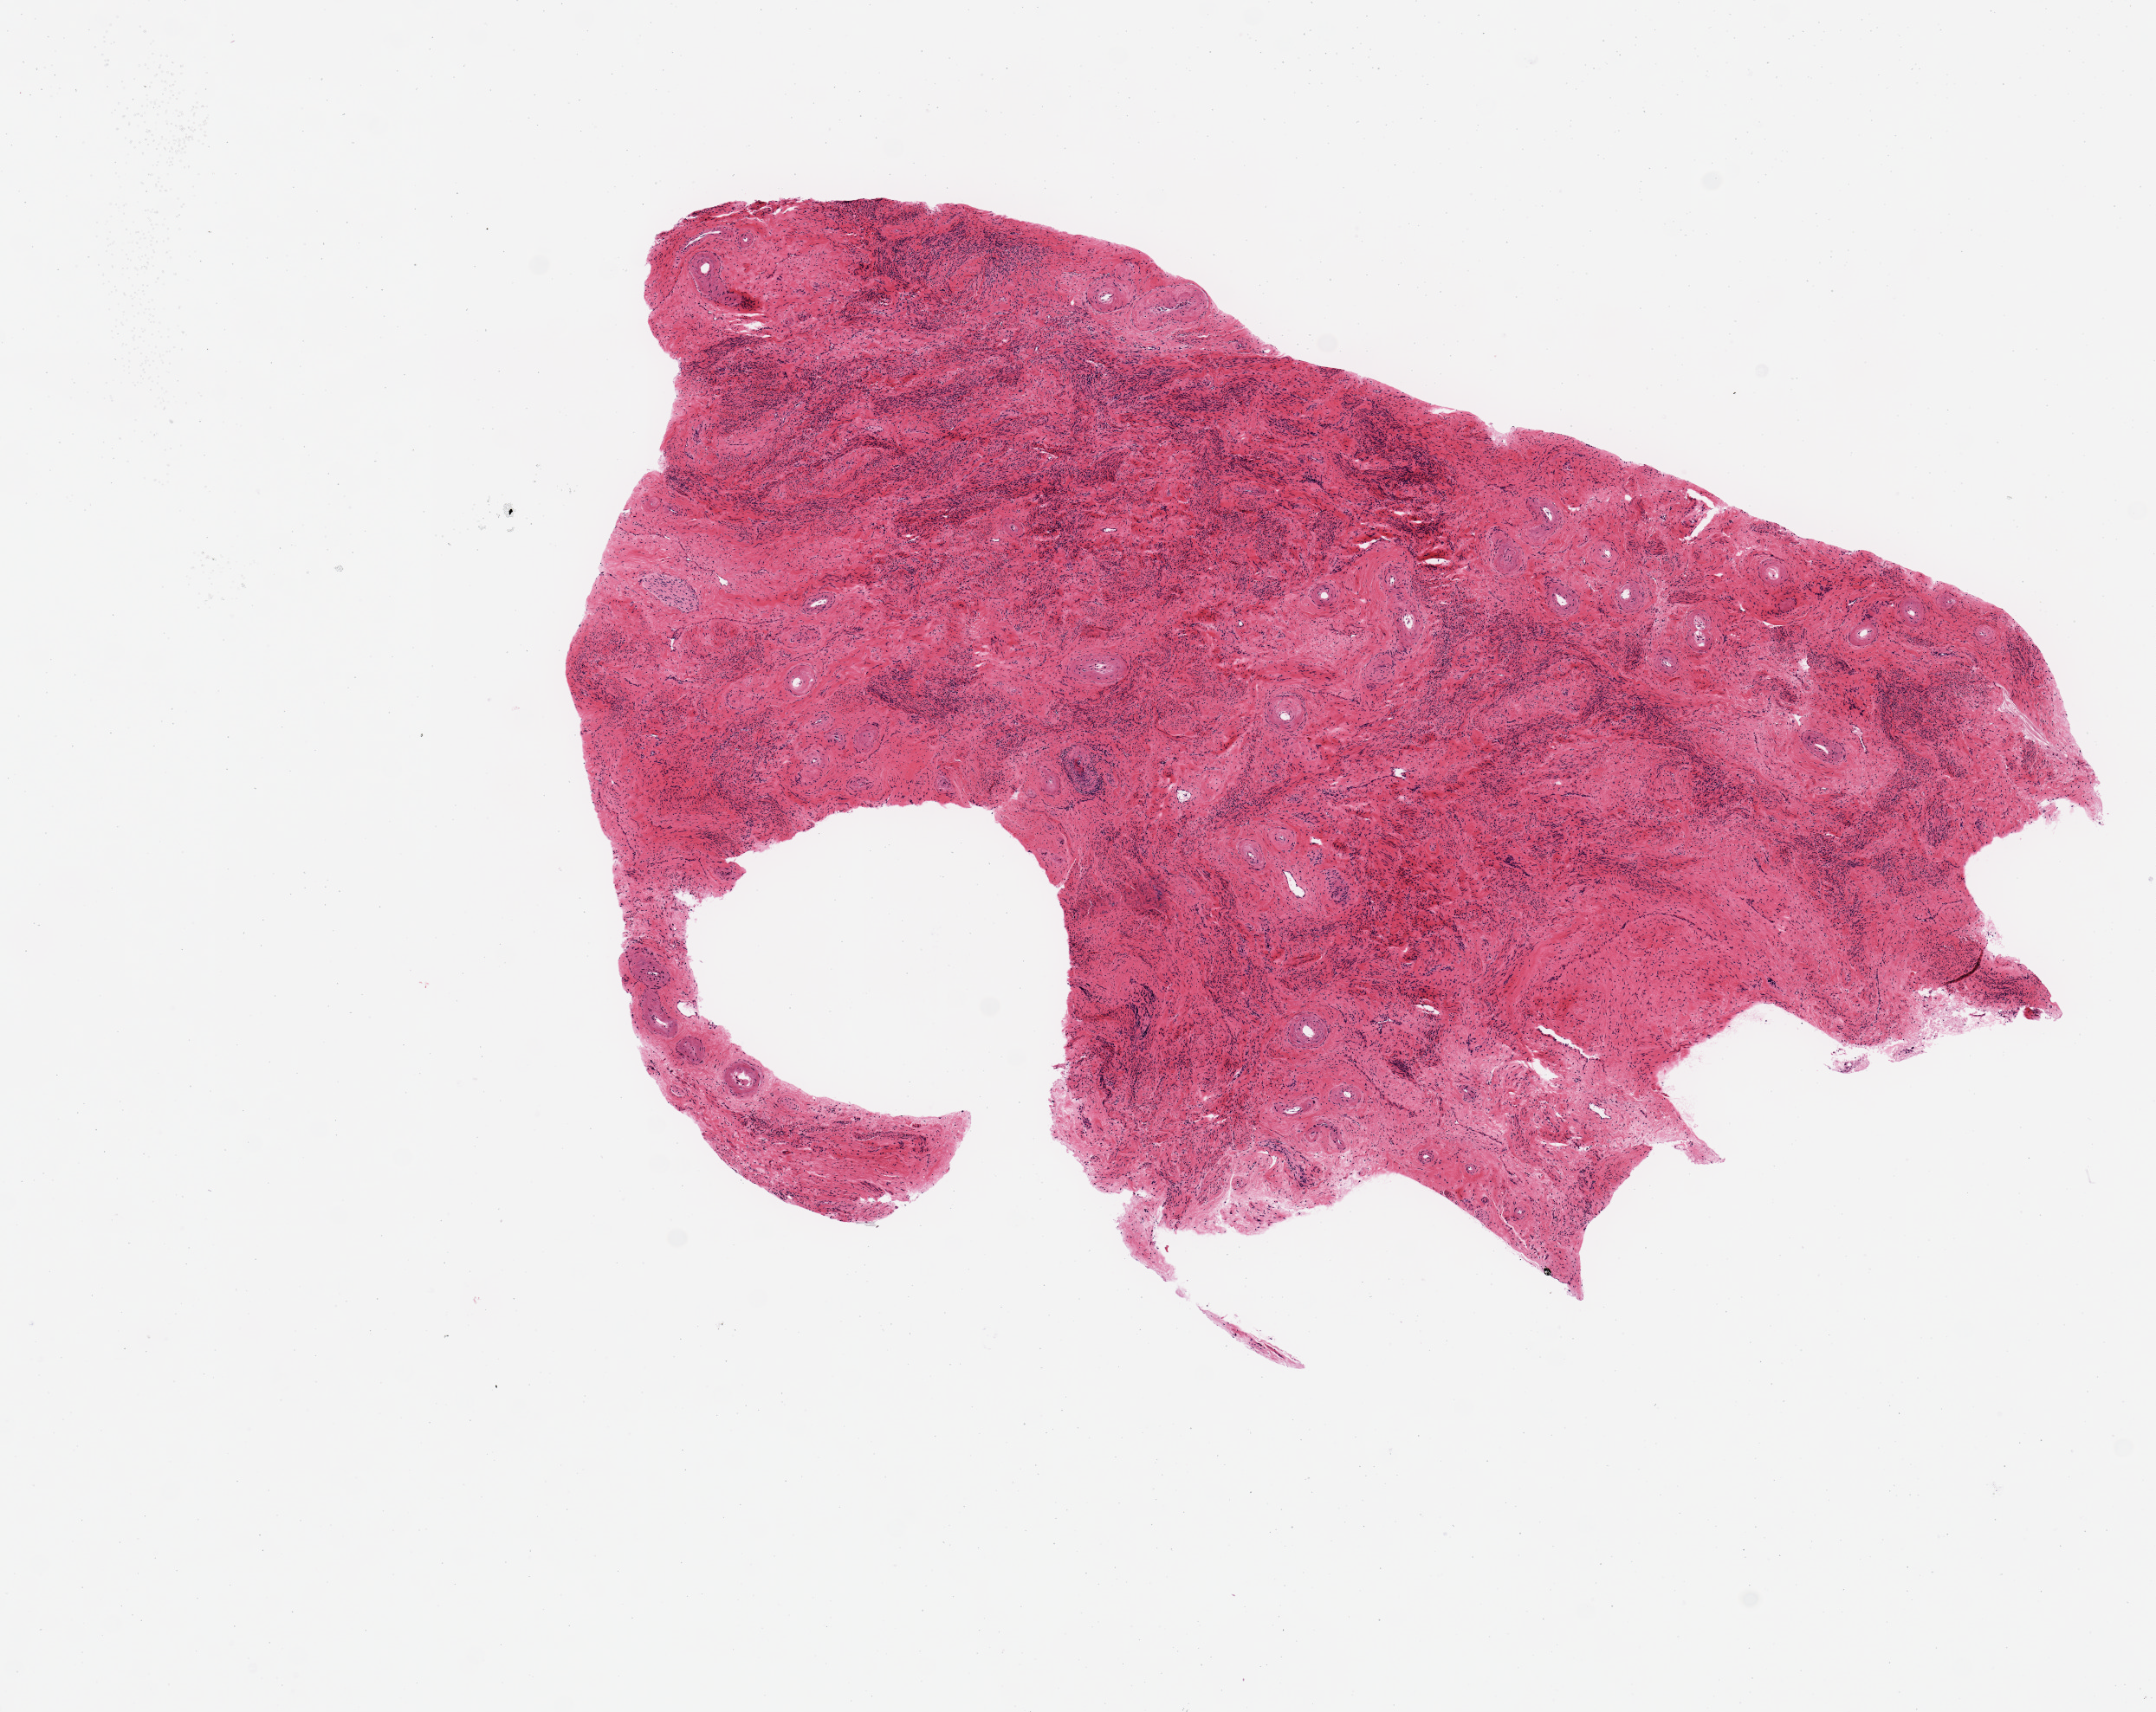
Haematoxylin and eosin whole-slide image, low-resolution overview of the scanned area, about 9.8 x 7.8 mm (slide scanned at 20x). PAXgene-fixed, paraffin-embedded tissue. Sampled site (target tissue): endocervix. Tissue donor sample. Female donor.
Pathologist's review note for this sample: 6x4 mm; cervical stroma without glands or surface.